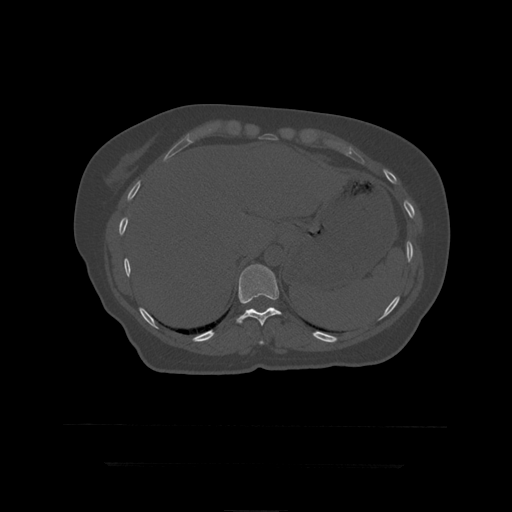
CT including the spine, one axial slice. Slice 219 of 399 in the series (ordered by position). Reconstruction kernel STANDARD. 120 kVp. Bone window (W 1800 / L 400 HU). 512 × 512 image matrix, field of view 450 × 450 mm. Patient age 41 years. From the clinical record (not read from this slice): primary cancer: breast.
Outlined on this slice (semi-automatic segmentation, software-assisted and operator-edited):
- T10 vertebra: bounding box [x1, y1, x2, y2] px = [259, 341, 264, 345]
- T11 vertebra: [236, 265, 283, 326]